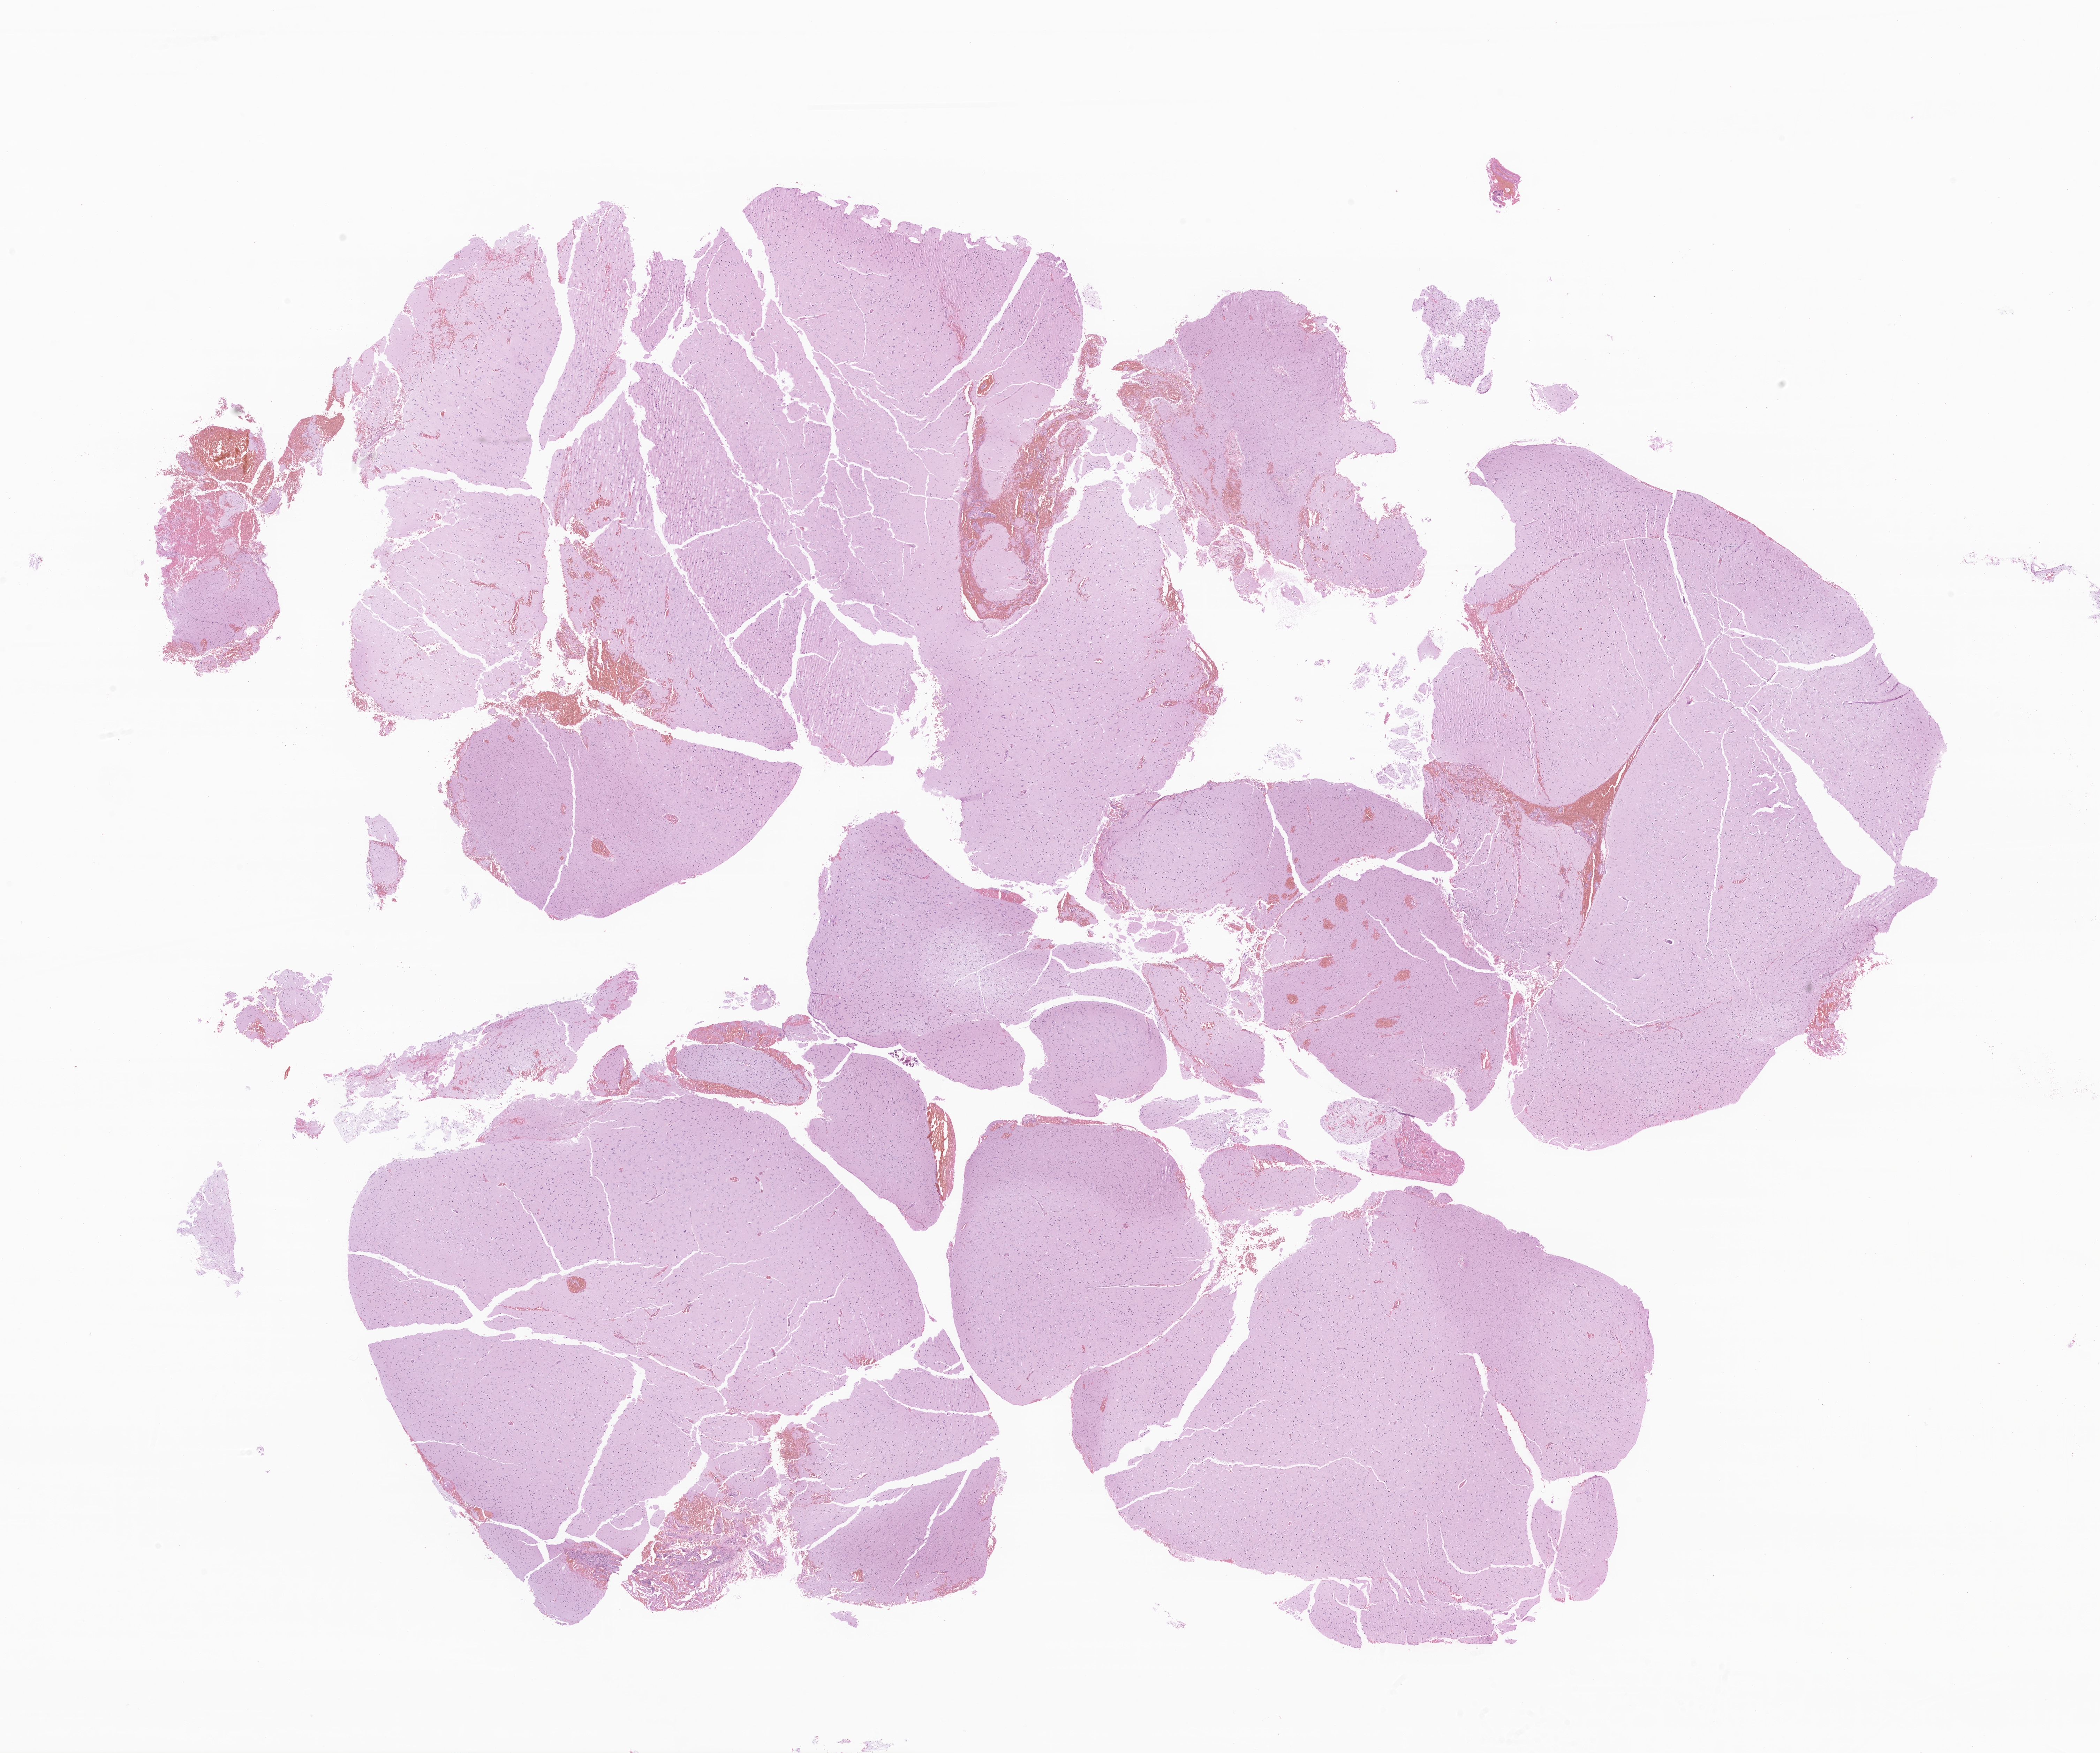
Whole-slide image, haematoxylin and eosin stain of tumor tissue from the brain, a low-resolution overview of the entire scanned area, about 25.4 x 21.2 mm. Formalin-fixed, paraffin-embedded (FFPE) tissue. Male patient, age 226 months (18 years 10 months).
Diagnosis (ICD-O-3 morphology term): Neoplasm, uncertain whether benign or malignant.